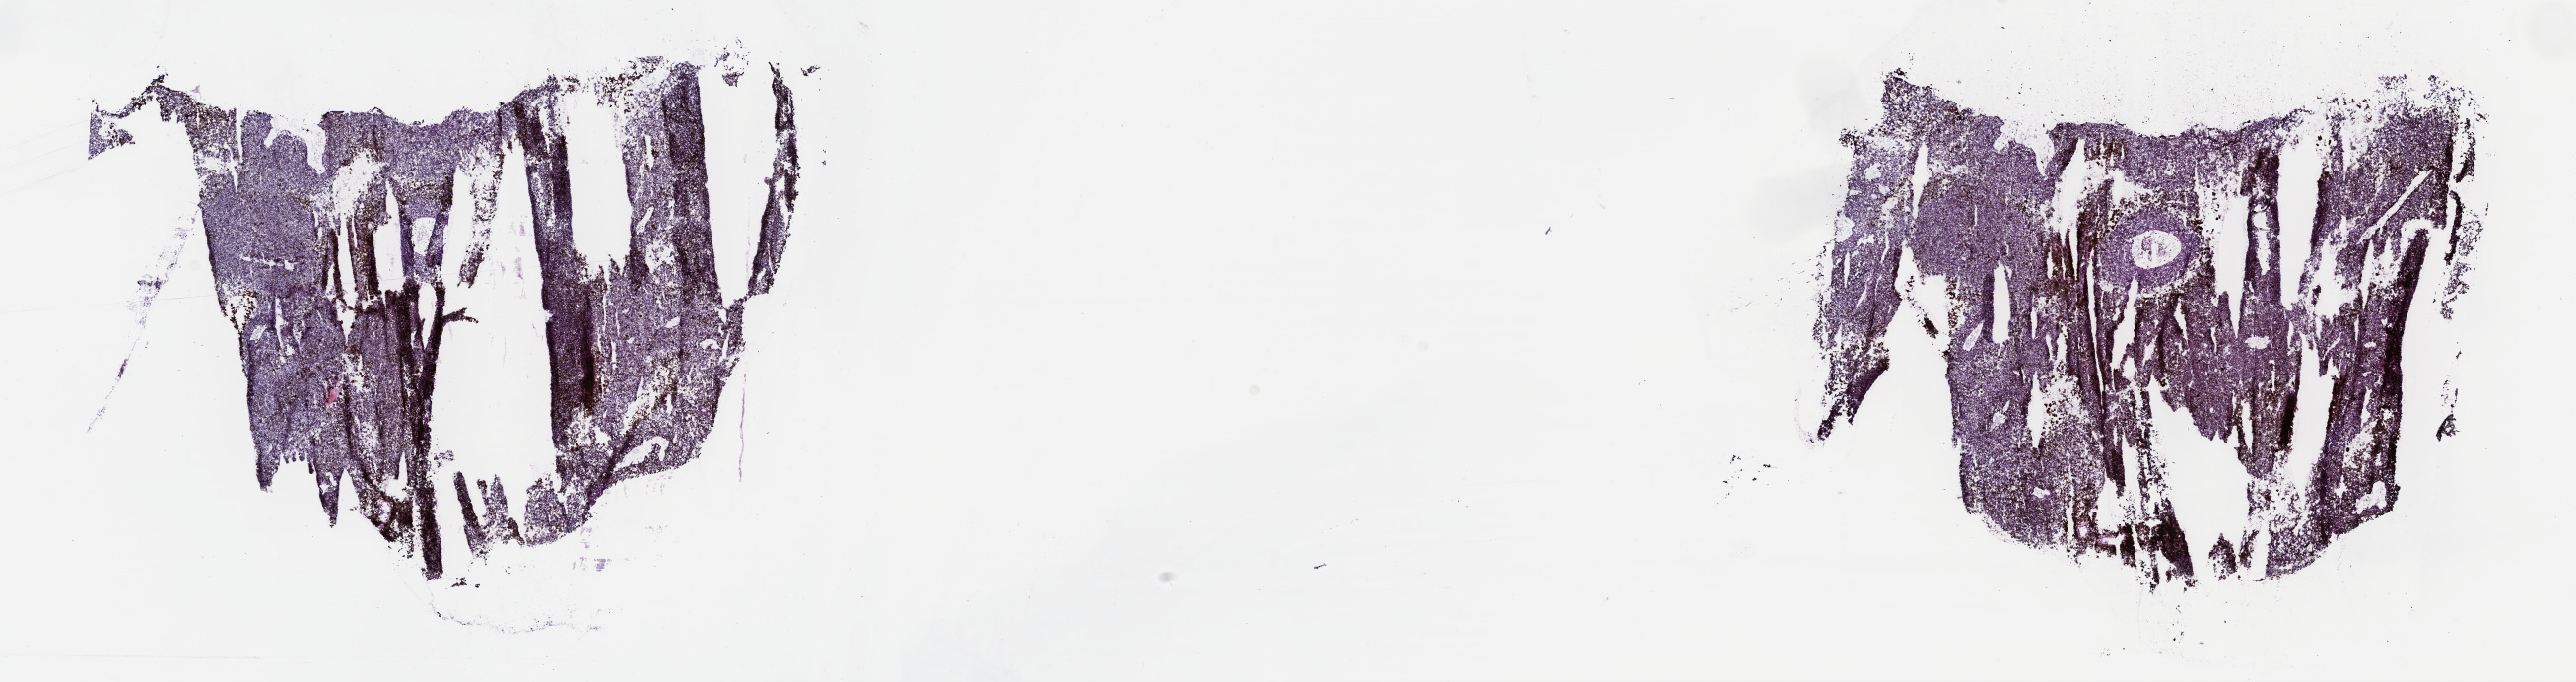
Hematoxylin and eosin (H&E) stained whole-slide image — low-resolution overview of the scanned area, about 21.1 x 5.6 mm, frozen section from the top of the tissue portion, uvea, primary tumour sample. Female patient; age at initial diagnosis 78 years. Composition of this section per pathologist review: tumour cells 100%, tumour nuclei 80%, normal cells 0%, stromal cells 0%, necrosis 0%. Infiltration values recorded for this section: lymphocyte infiltration 1%, monocyte infiltration 0%, neutrophil infiltration 0%.
* TNM: T3a N0 M0
* pathologic diagnosis: Mixed epithelioid and spindle cell melanoma (choroid)
* AJCC pathologic stage: IIB (7th edition)